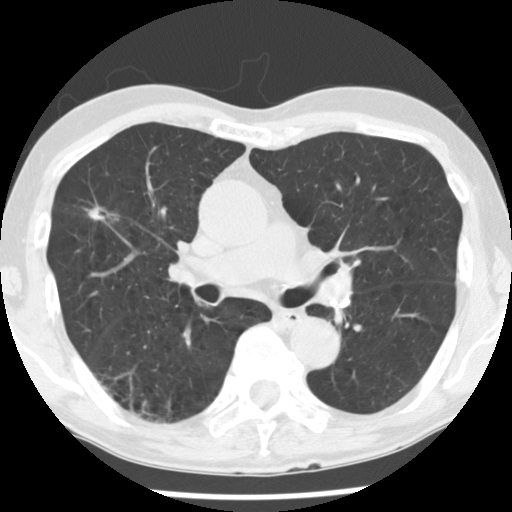
Chest CT (low-dose screening protocol), one axial image. First (baseline) screen. Lung window (W 1500 / L -600 HU). 2.5 mm slice thickness. 120 kVp. 512 × 512 image matrix. Male, age 72 years at enrolment. Current smoker at enrolment.
Lesion marked by an expert reader, box from (x=77, y=194) to (x=131, y=240) px. Screening reader's record for this exam (one nodule recorded; not confirmed to be the boxed lesion): non-calcified nodule or mass ≥4 mm, right upper lobe, 11 × 8 mm, spiculated (stellate) margins, soft tissue attenuation. Official screen result: positive, change unspecified: nodule(s) >= 4 mm or enlarging nodule(s), mass(es), or other non-specific abnormalities suspicious for lung cancer. Lung cancer was diagnosed 72 days after this screen: bronchiolo-alveolar adenocarcinoma, NOS, right upper lobe, moderately differentiated (G2), stage IA (AJCC 6th edition), 10 mm at pathology.